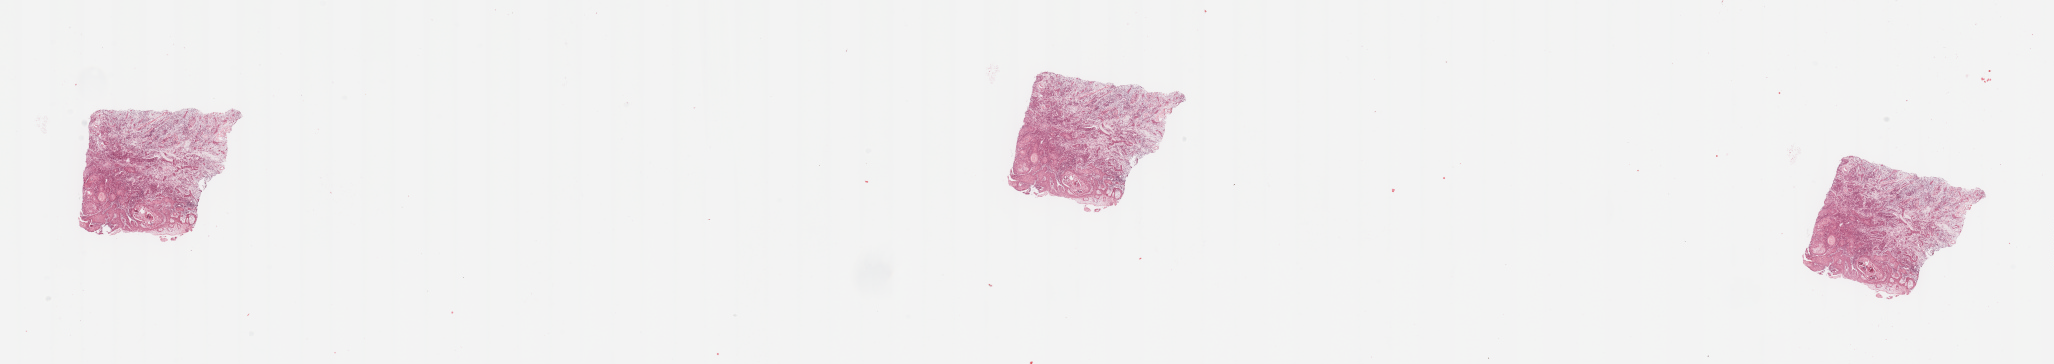
H&E whole-slide image, whole scanned area (about 32.5 x 5.8 mm, slide scanned at 20x) shown as a low-resolution overview, tumour tissue sample, sampled site: tongue. Male, 57 y/o. Histologic grade: G2 (moderately differentiated). Slide review estimates, as recorded: tumour nuclei 80%, necrosis 5%.
- histologic diagnosis: Squamous cell carcinoma, NOS (tongue, NOS)
- AJCC pathologic stage: IVA